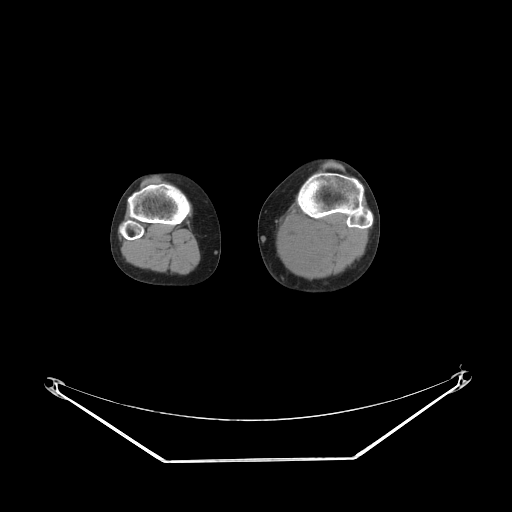
CT of an extremity soft-tissue mass (from a PET/CT study), one axial slice. Position 158 of 223 along the scan axis. Soft-tissue window (W 400 / L 40 HU). 512 × 512 image matrix, field of view 500 × 500 mm. Female patient. From the clinical record (not read from this slice): histological type: extraskeletal high grade osteogenic sarcoma; grade: high; site of the primary tumour: left calf.
Structures marked on this image (expert contour drawn on MRI and transferred to this co-registered scan by the dataset authors):
- gross tumour volume (mass): bounding box (x1, y1, x2, y2) in pixels: (279, 226, 337, 270)